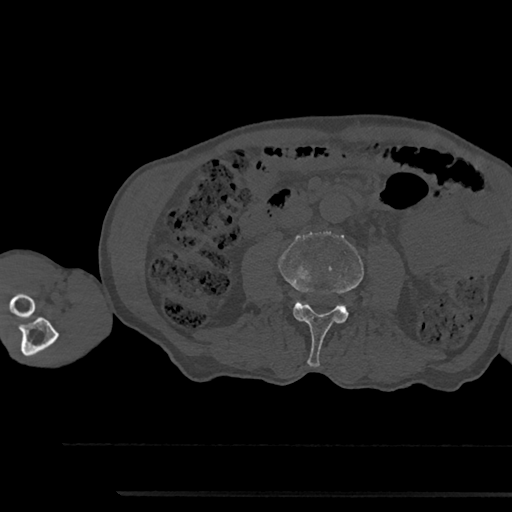
CT including the spine, one axial slice; position 476 of 797 along the scan axis; reconstruction kernel Br40s/3; 120 kVp; bone window (W 1800 / L 400 HU); 512 × 512 image matrix, field of view 367 × 367 mm. Male patient, age 79 years. From the clinical record (not read from this slice): primary cancer: prostate.
Structures marked on this image (semi-automatic segmentation, software-assisted and operator-edited):
- L3 vertebra: bounding box (x1, y1, x2, y2) in pixels: (279, 232, 364, 367)